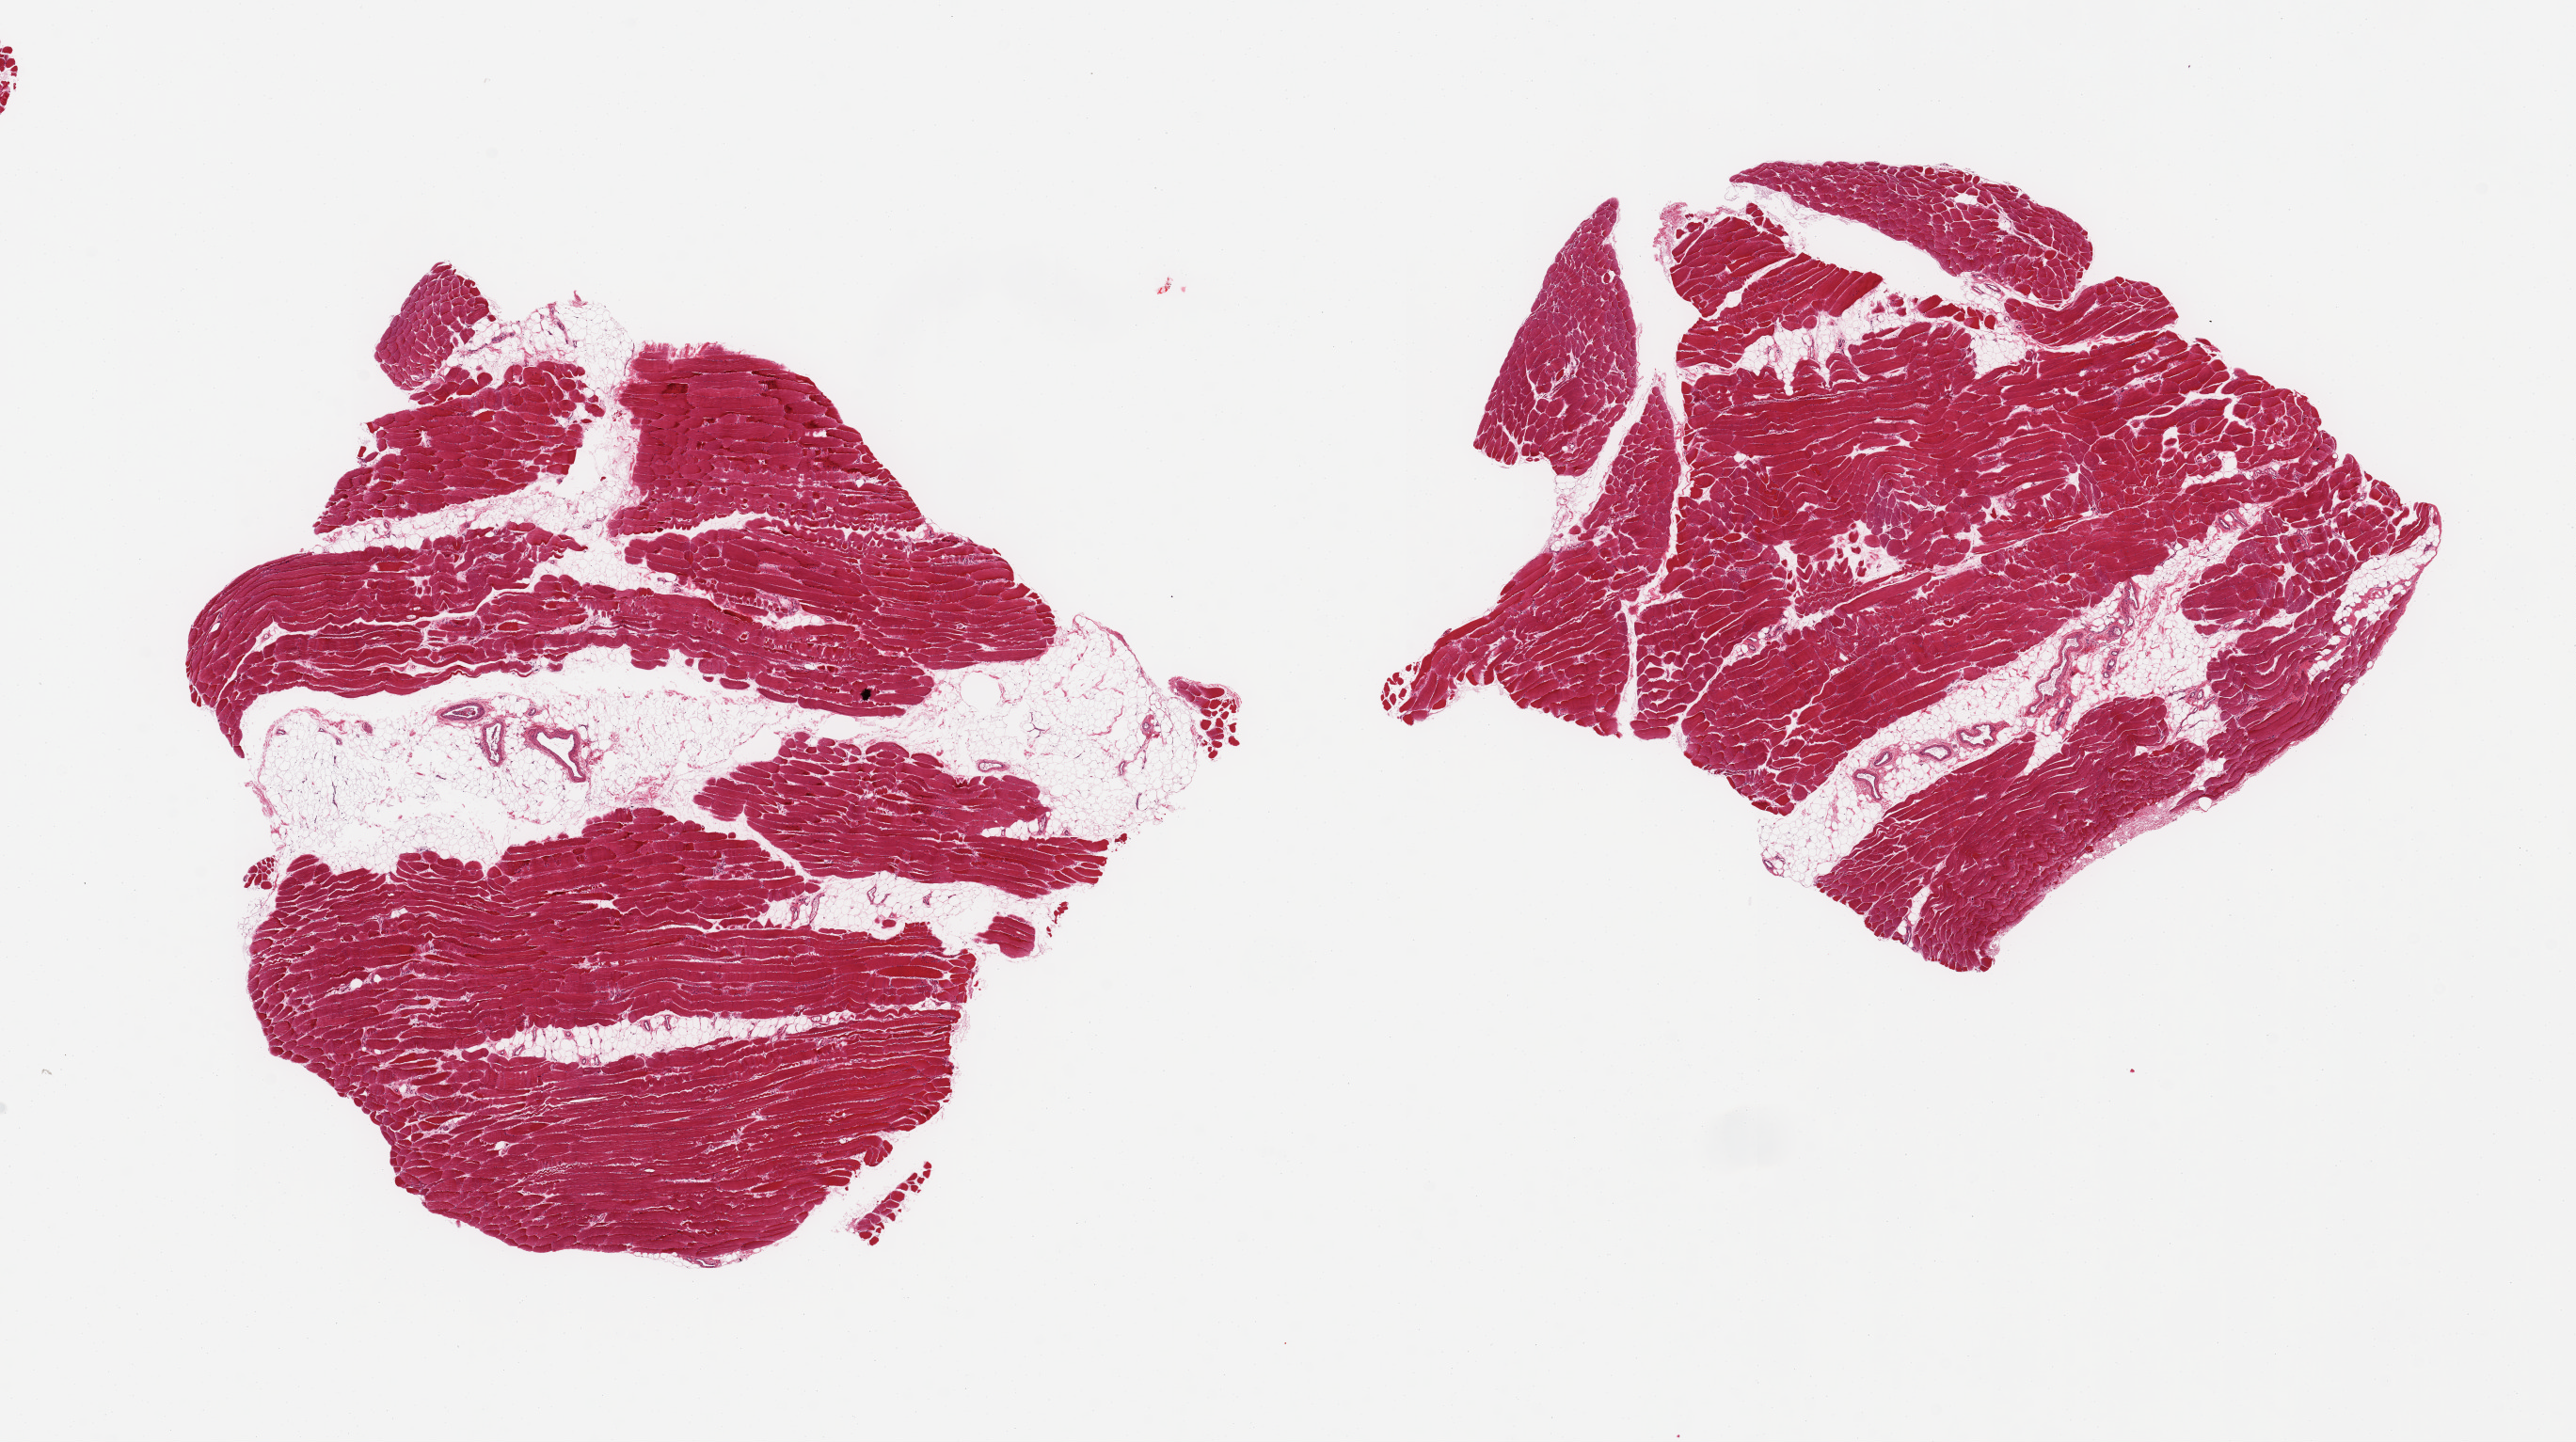
Whole-slide image, haematoxylin and eosin stain, a low-resolution overview of the entire scanned area, about 21.7 x 12.1 mm (from a 20x scan), PAXgene-fixed paraffin-embedded (PFPE) section, sampled site (target tissue): skeletal muscle, tissue donor sample. Male donor.
- reviewer comment on this tissue sample: 2 pieces, ~20% interstitial fat/vascular elements